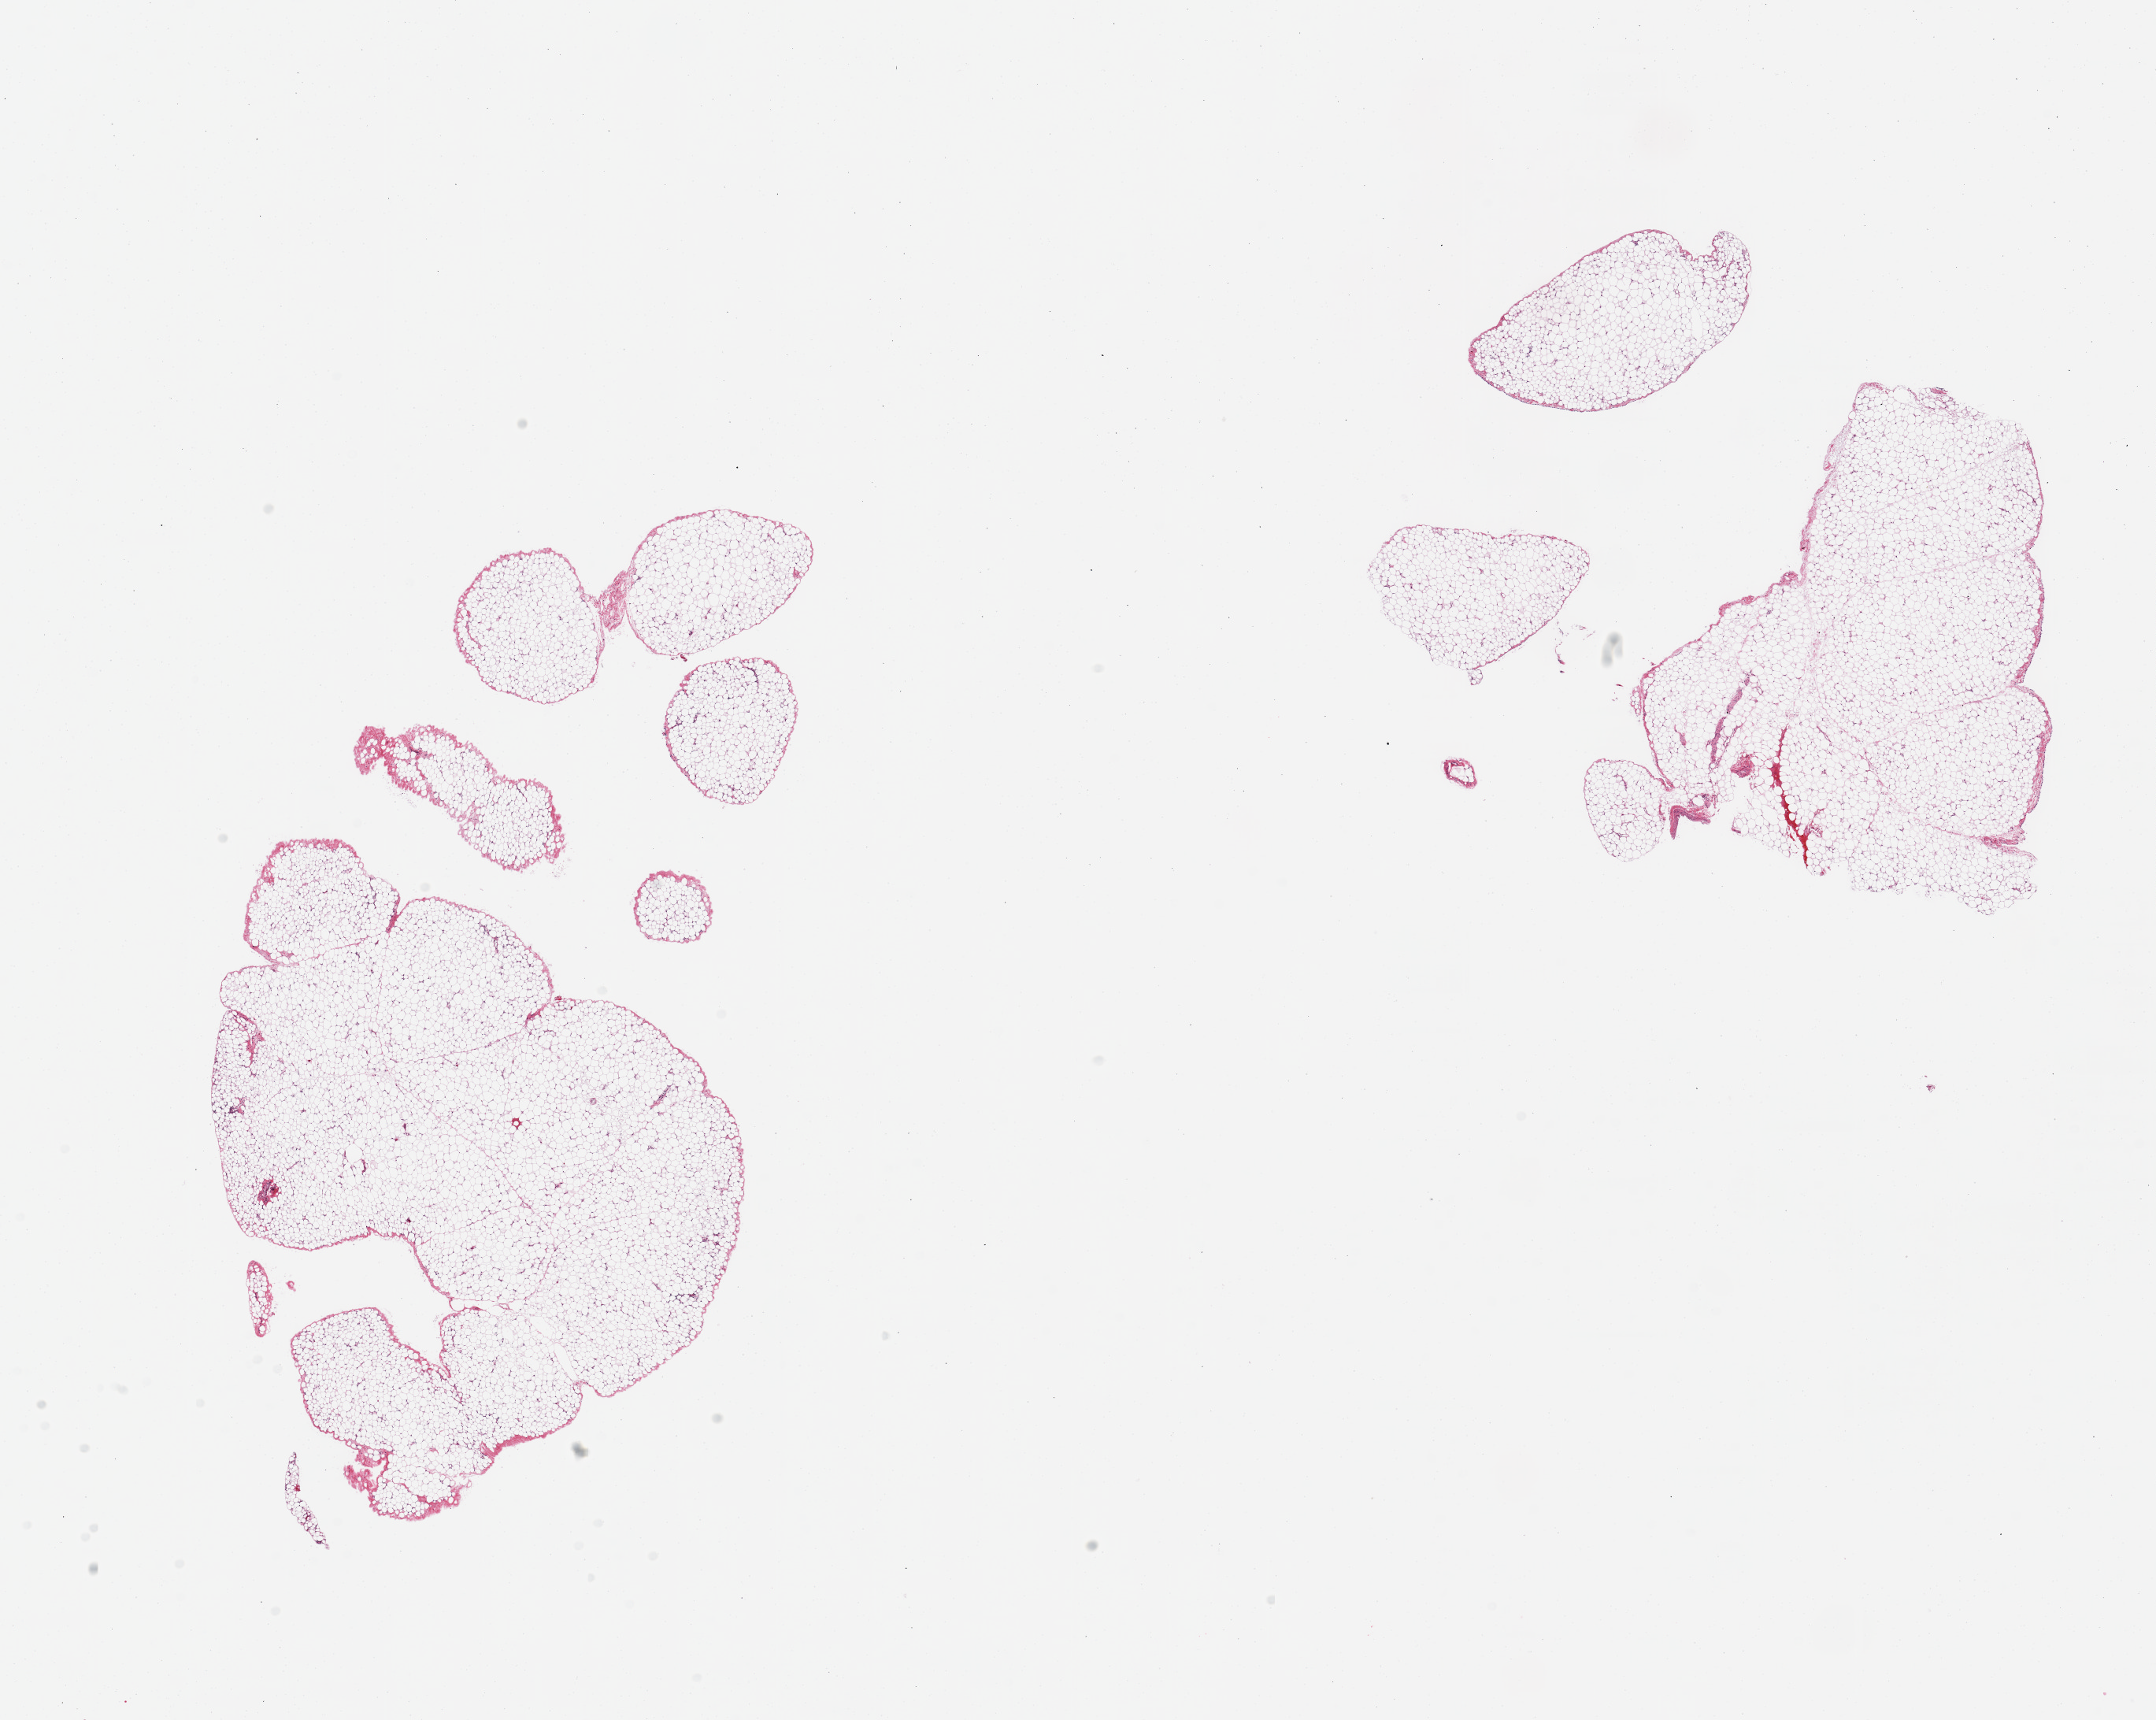
Whole-slide image, H&E stain, brightfield — low-resolution overview of the scanned area, about 21.7 x 17.3 mm (from a 20x scan). PAXgene-fixed, paraffin-embedded tissue. Section of omentum (target tissue). Tissue donor sample. Female donor.
• review note (as recorded): 2 fragmented pieces; lobulated mature adipose tissue